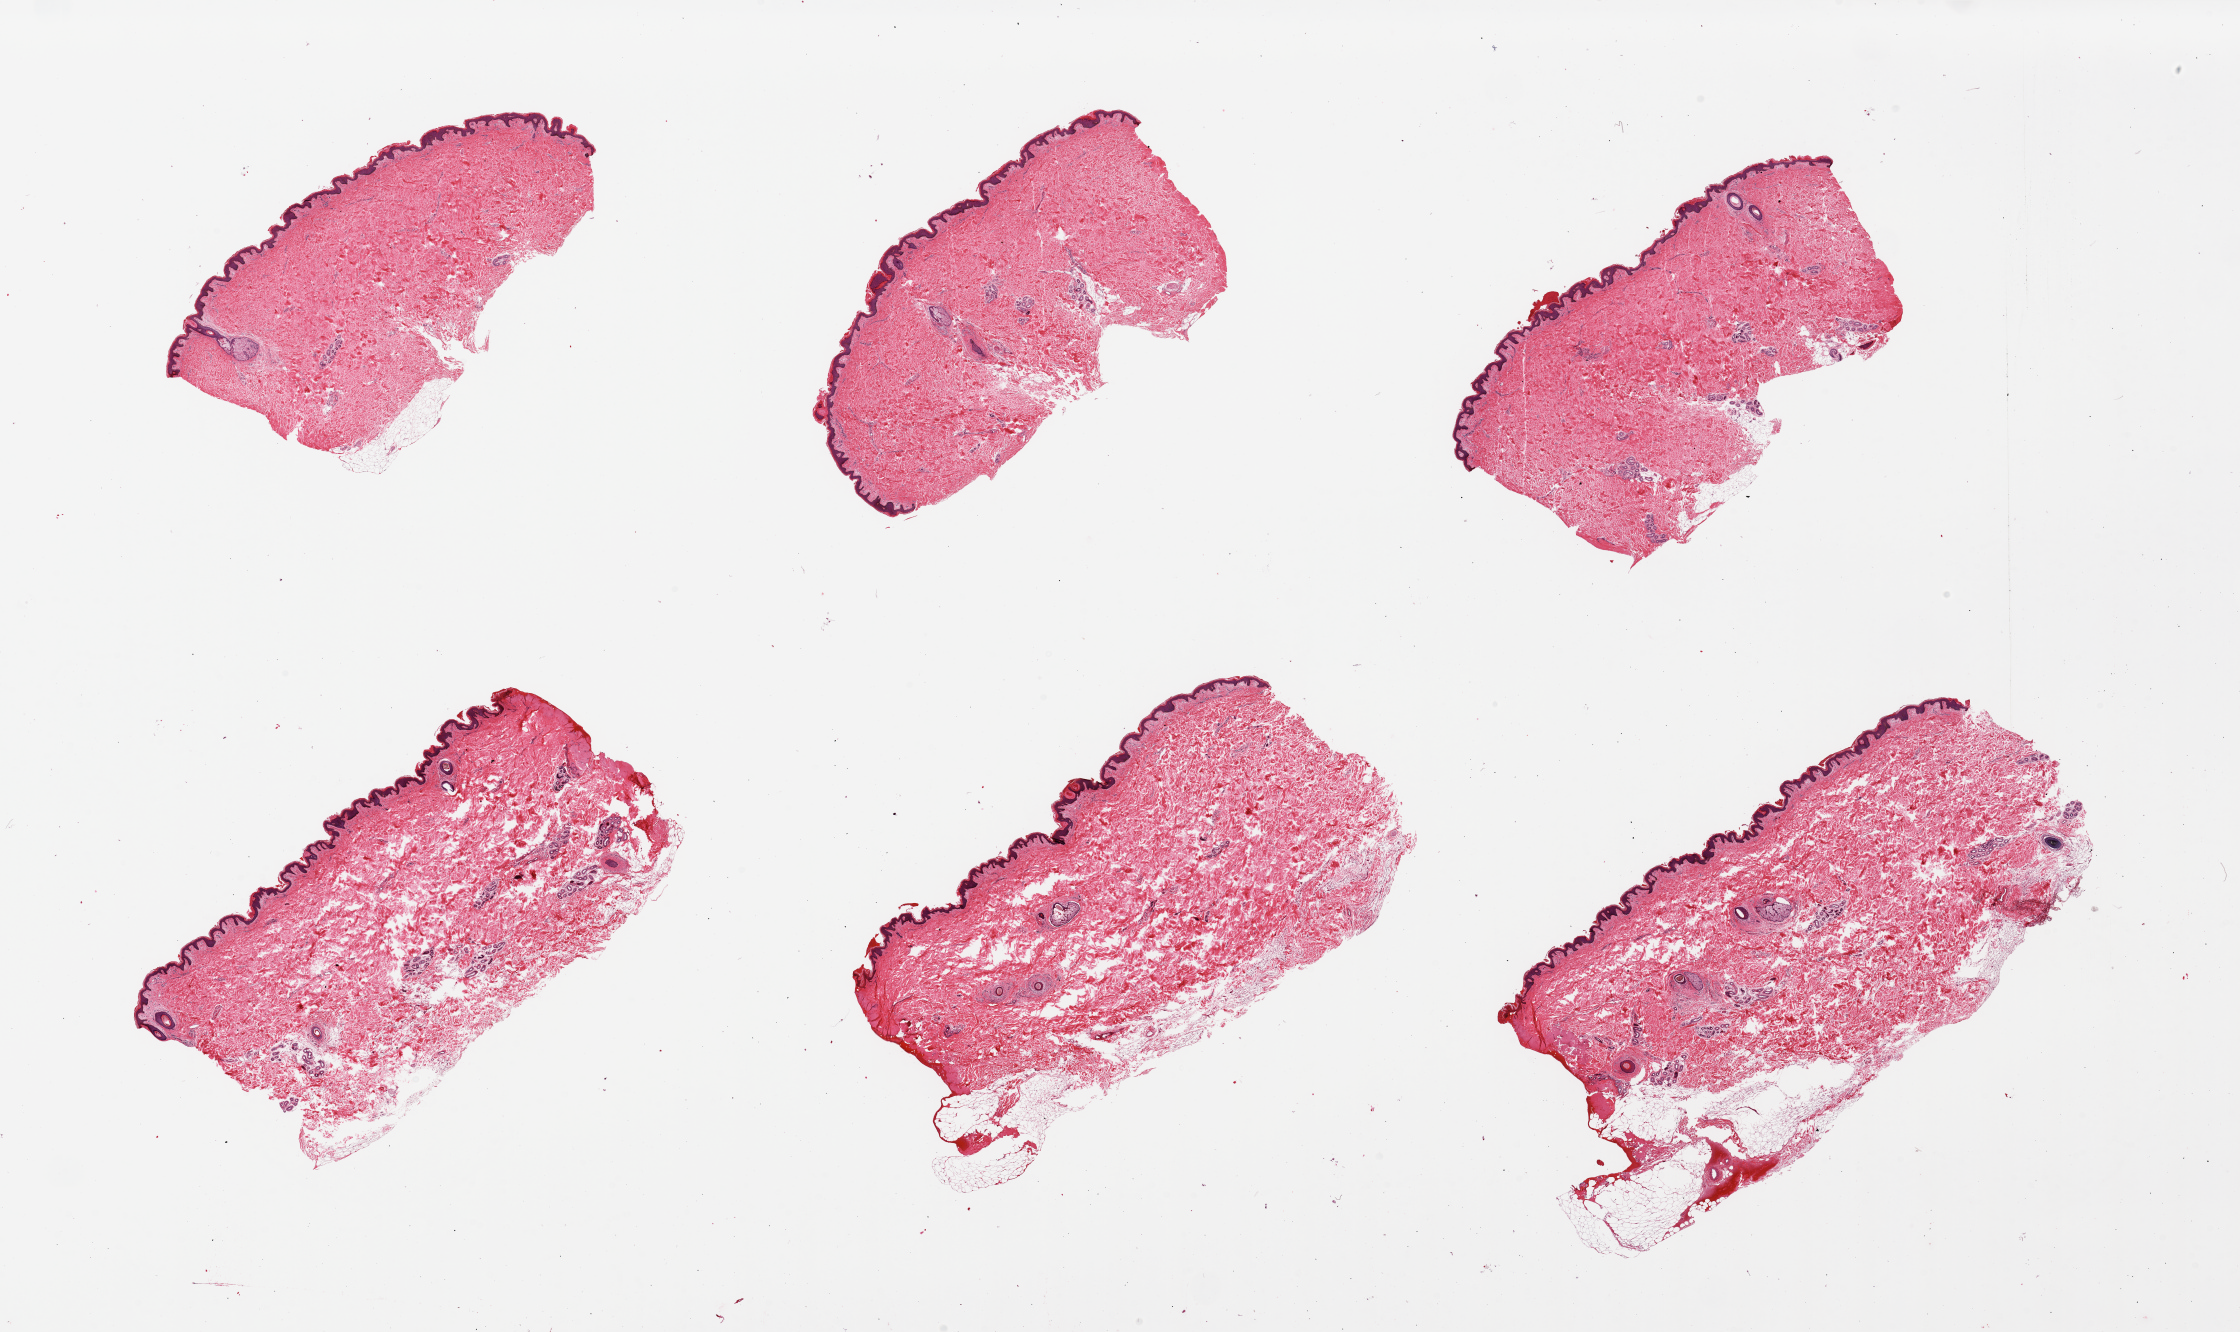
Hematoxylin and eosin (H&E) whole-slide image, shown as a low-resolution overview of the whole scanned area (about 35.4 x 21.1 mm), PAXgene-fixed paraffin-embedded (PFPE) section, section of skin of suprapubic region (target tissue), donor tissue sample. Donor: male.
Pathologist's review note for this sample: 6 pieces. Squamous epithelium is ~1.5% thickness. Minimal dermal fat.